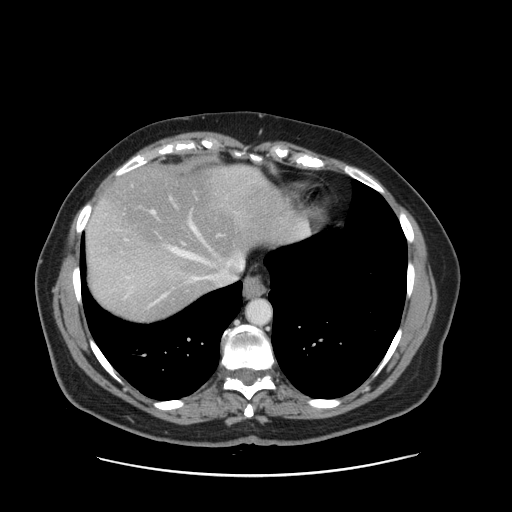
Contrast-enhanced abdominal CT, one axial slice; position 131 of 161 along the scan axis; 120 kVp; intravenous contrast given; soft-tissue window (W 400 / L 40 HU); 512 × 512 image matrix. Female patient, age 62 years. Case-level facts recorded for this patient, not image findings: diagnosis: colorectal cancer liver metastases, imaged before liver resection; multiple liver metastases: no; largest metastasis: 2.5 cm; disease in both lobes: no.
Annotated regions visible in this slice (manually delineated by an expert):
- hepatic veins: box from (x=126, y=173) to (x=254, y=290) px
- liver: (x=86, y=165)–(x=303, y=321)
- planned liver remnant (the part of the liver to remain after resection): (x=95, y=166)–(x=304, y=279)
- portal vein (with intrahepatic branches): (x=151, y=196)–(x=221, y=244)